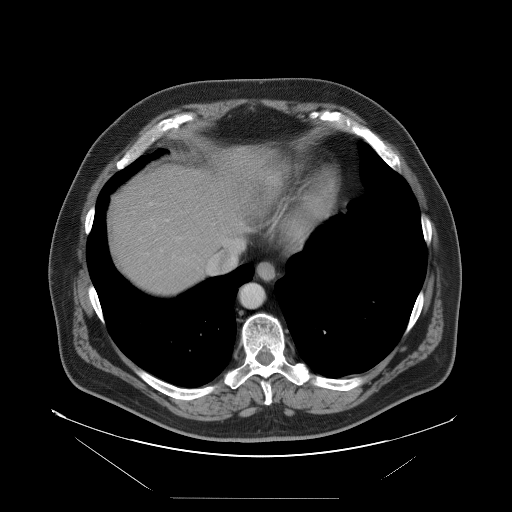
Contrast-enhanced abdominal CT, one axial slice; slice 89 of 114 in the series (ordered by position); 120 kVp; intravenous contrast given; soft-tissue window (W 400 / L 40 HU); 5 mm slice thickness; 512 × 512 image matrix. Male patient, age 61 years. From the clinical record (not read from this slice): diagnosis: colorectal cancer liver metastases, imaged before liver resection; multiple liver metastases: no; largest metastasis: 6.5 cm.
Annotated regions visible in this slice (outlined manually by an expert reader):
- hepatic veins: bounding box [x1, y1, x2, y2] px = [207, 234, 243, 274]
- liver: [109, 150, 273, 295]
- planned liver remnant (the part of the liver to remain after resection): [160, 161, 246, 252]